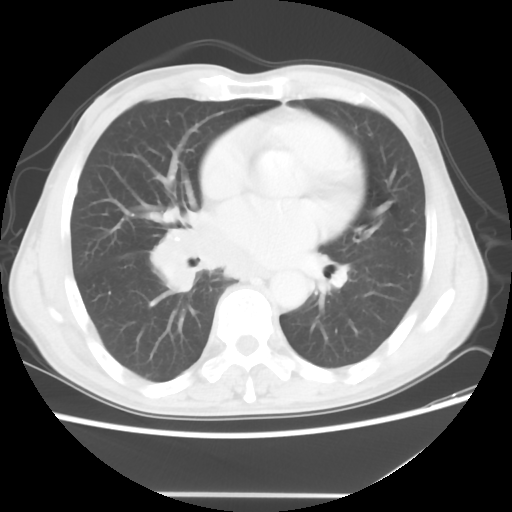
Chest CT, one axial slice. Slice 25 of 56 in the series (ordered by position). Reconstruction kernel STANDARD. 120 kVp. Lung window (W 1500 / L -600 HU). 5 mm slice thickness. 512 × 512 image matrix, field of view 344 × 344 mm. Male patient, age 65 years. From the clinical record (not read from this slice): clinical TNM (as recorded): T1c N3 M0; histopathological grade: G3.
Outlined on this slice (bounding box drawn by a radiologist):
- lung tumour (recorded histology: small cell carcinoma): box from (x=147, y=221) to (x=272, y=295) px